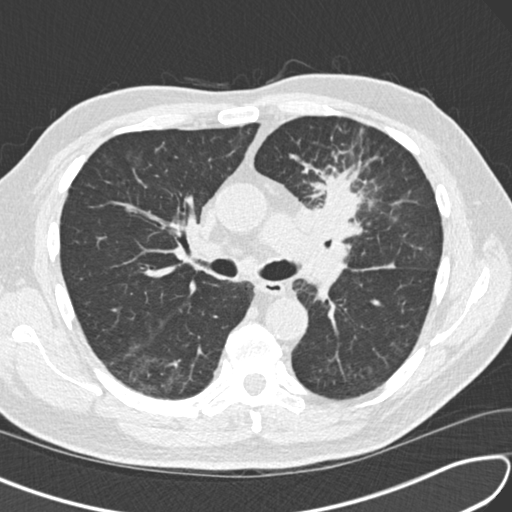
Low-dose screening chest CT, one axial slice. Position 95 of 156 along the scan axis. Reconstruction kernel B30f. 120 kVp. Lung window (W 1500 / L -600 HU). 512 × 512 image matrix, field of view 340 × 340 mm.
Annotated regions visible in this slice (manually delineated by an expert):
- lesion 1 (tumor, upper lobe of left lung): bounding box (x1, y1, x2, y2) in pixels: (317, 177, 359, 238)